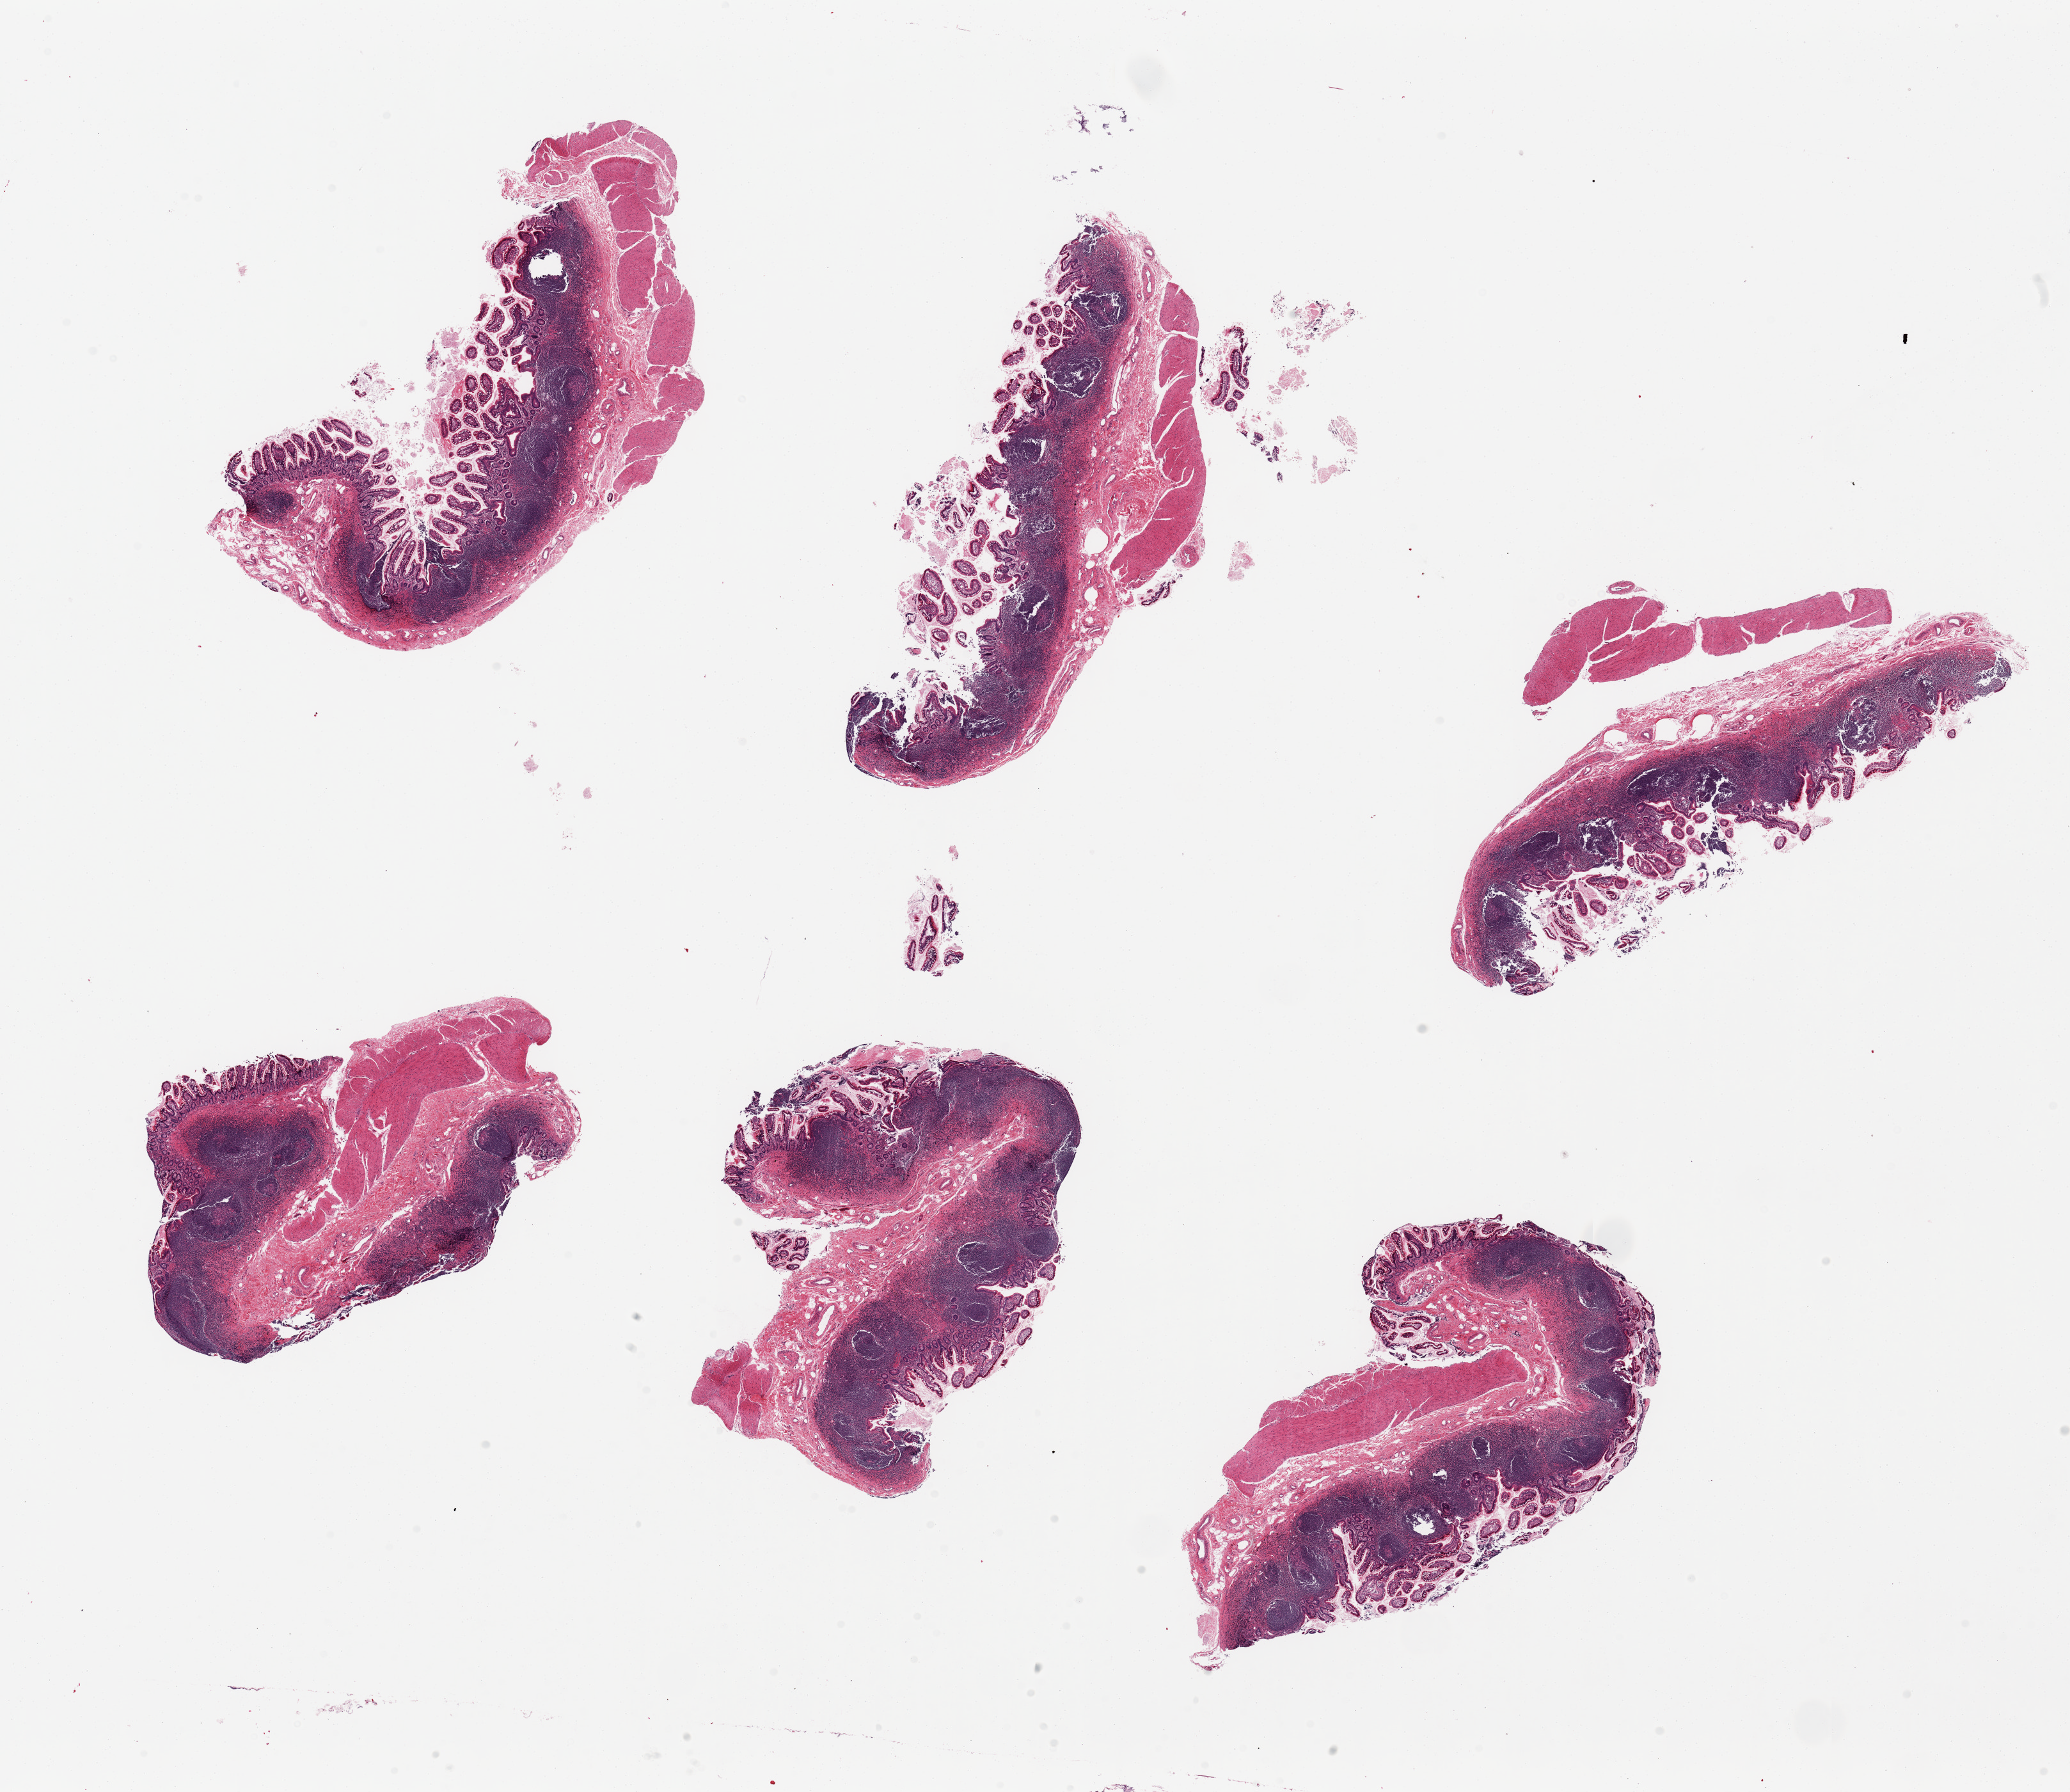
Whole-slide image, hematoxylin and eosin (H&E) stain — low-resolution overview of the scanned area, about 25.6 x 22.2 mm (slide scanned at 20x); PAXgene-fixed paraffin-embedded (PFPE) section; target tissue: ileum; tissue donor sample. Donor: female.
Reviewer comment on this tissue sample: 6 pieces, 7.5x4mm; well prserved, ~40% lymphoid elements; Superb specimen.